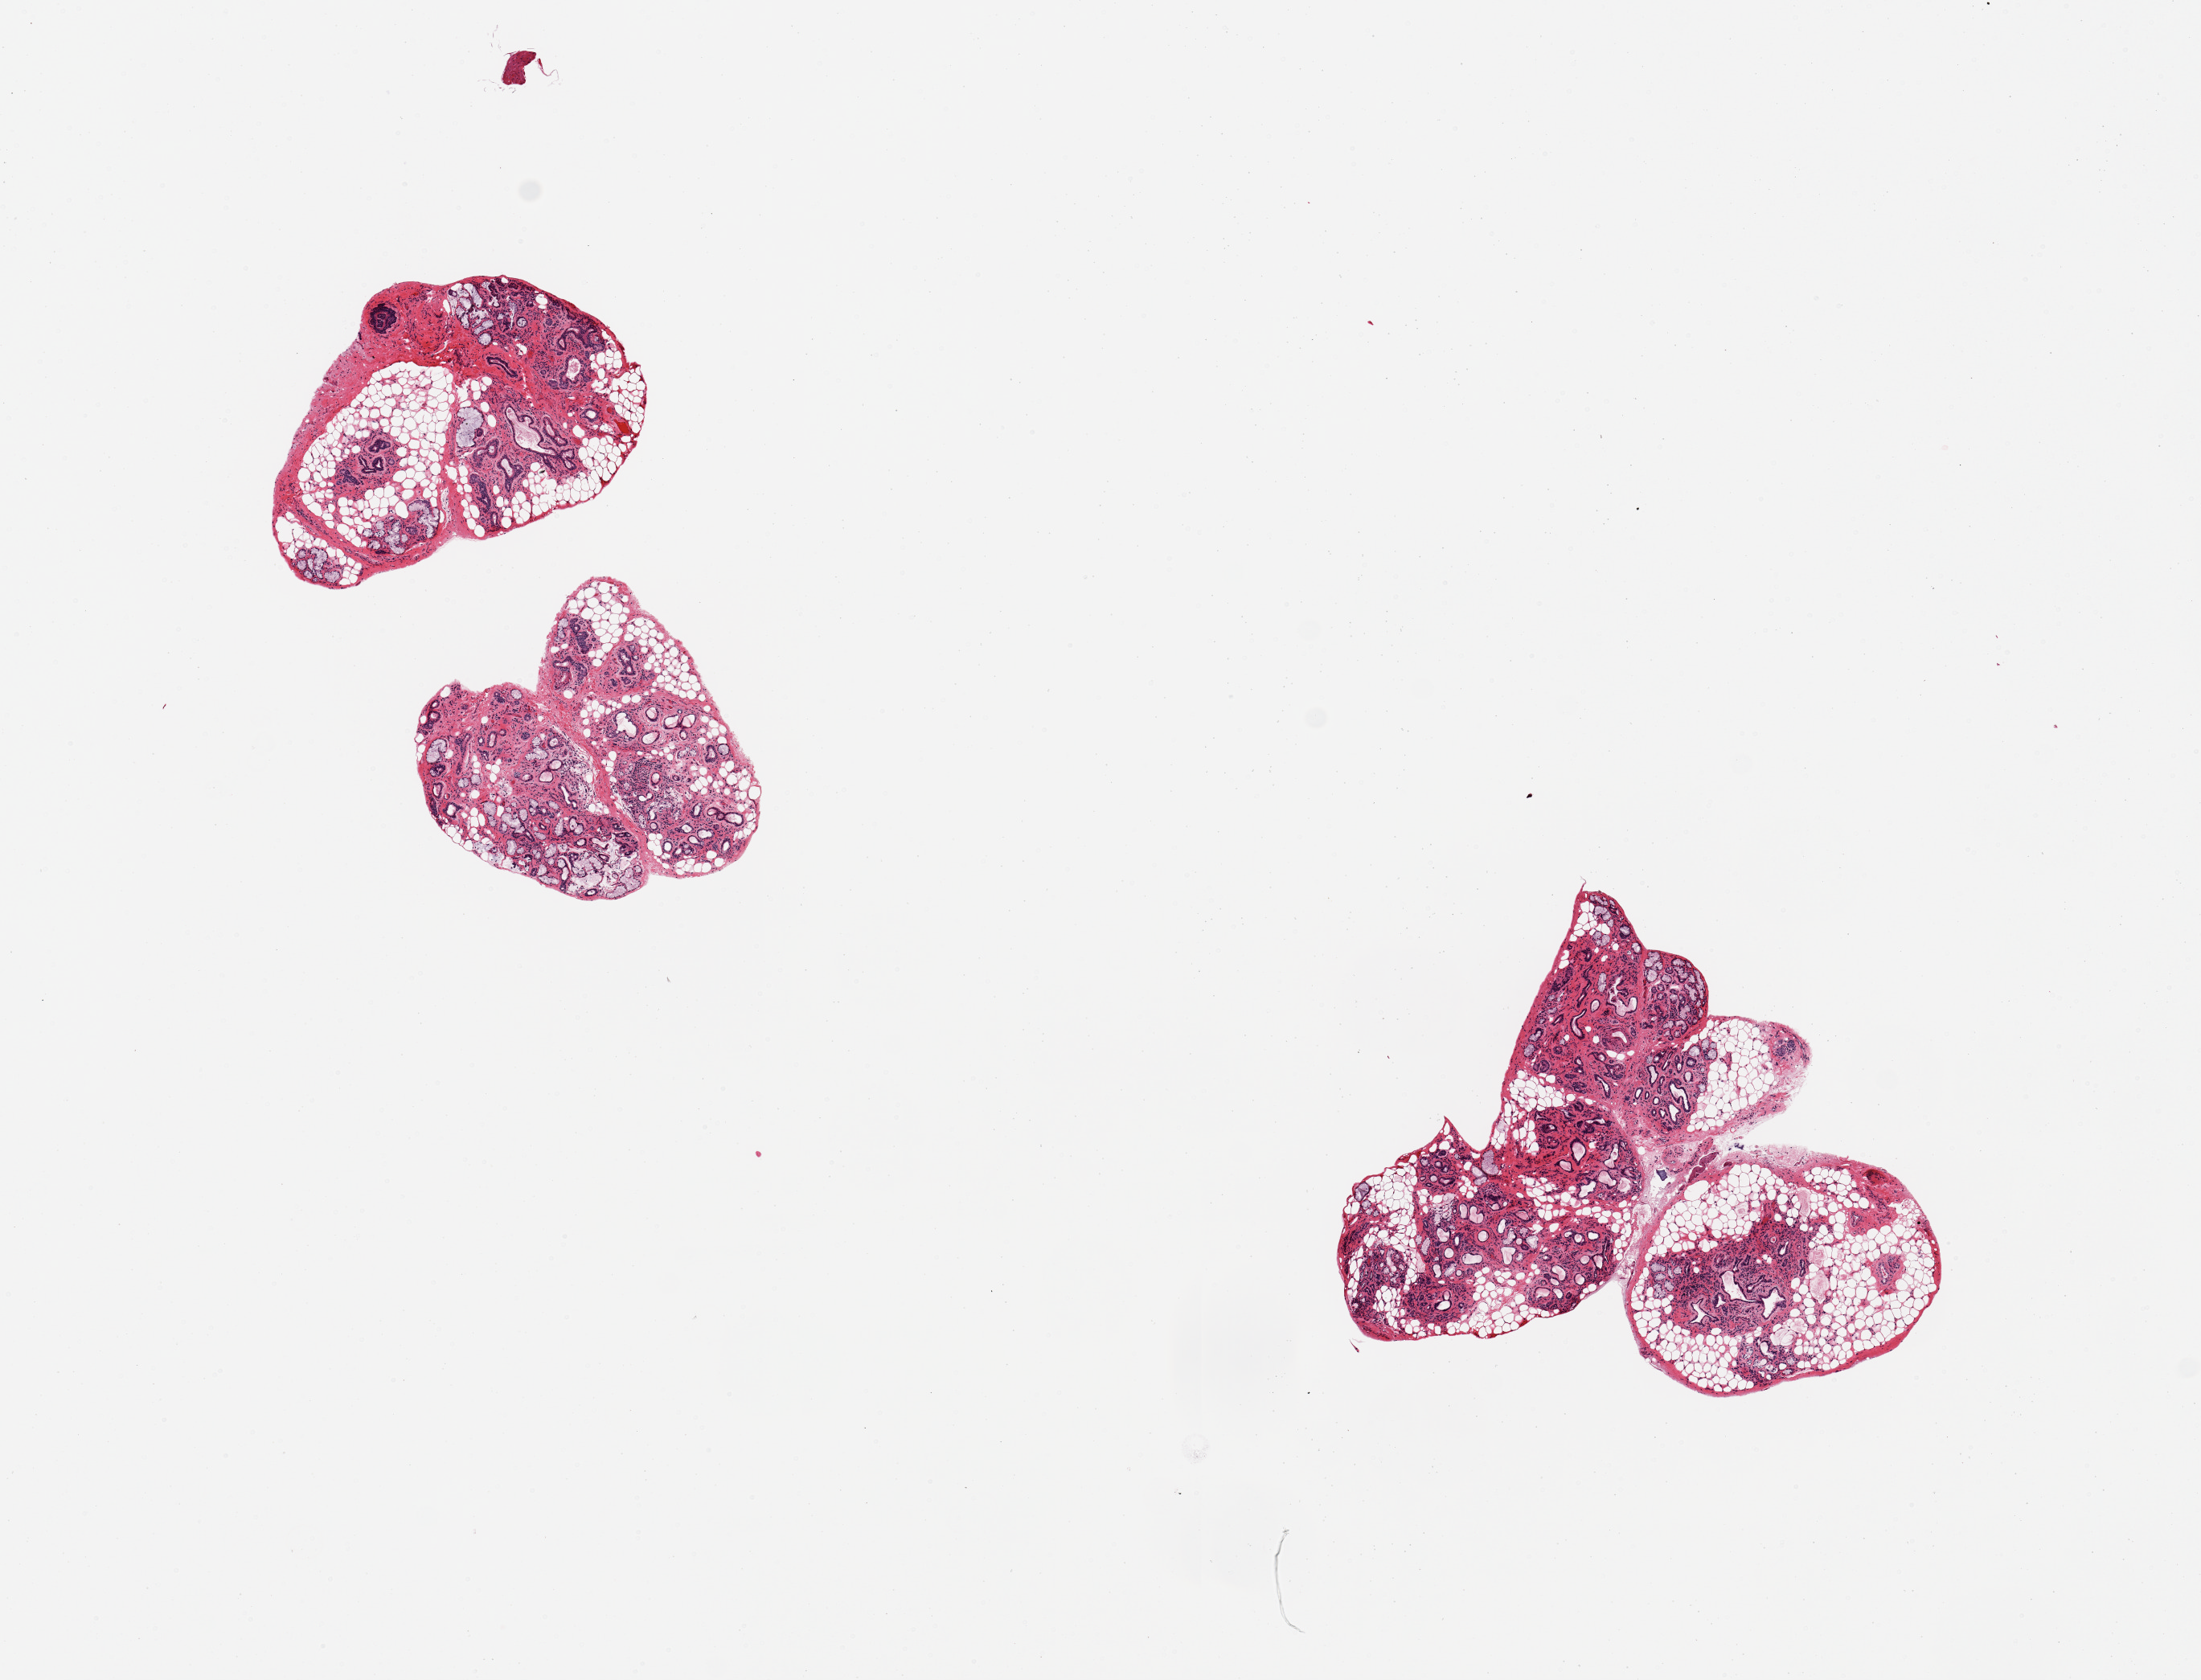
Whole-slide image, H&E stain, shown as a low-resolution overview of the whole scanned area (about 10.8 x 8.3 mm, slide scanned at 20x); PAXgene-fixed, paraffin-embedded tissue; target tissue: minor salivary gland; tissue donor sample.
Reviewer comment on this tissue sample: 3 pieces; chronic sialadenitis with fibrosis, atrophy, and minimal chronic inflammation; ~30% fat.